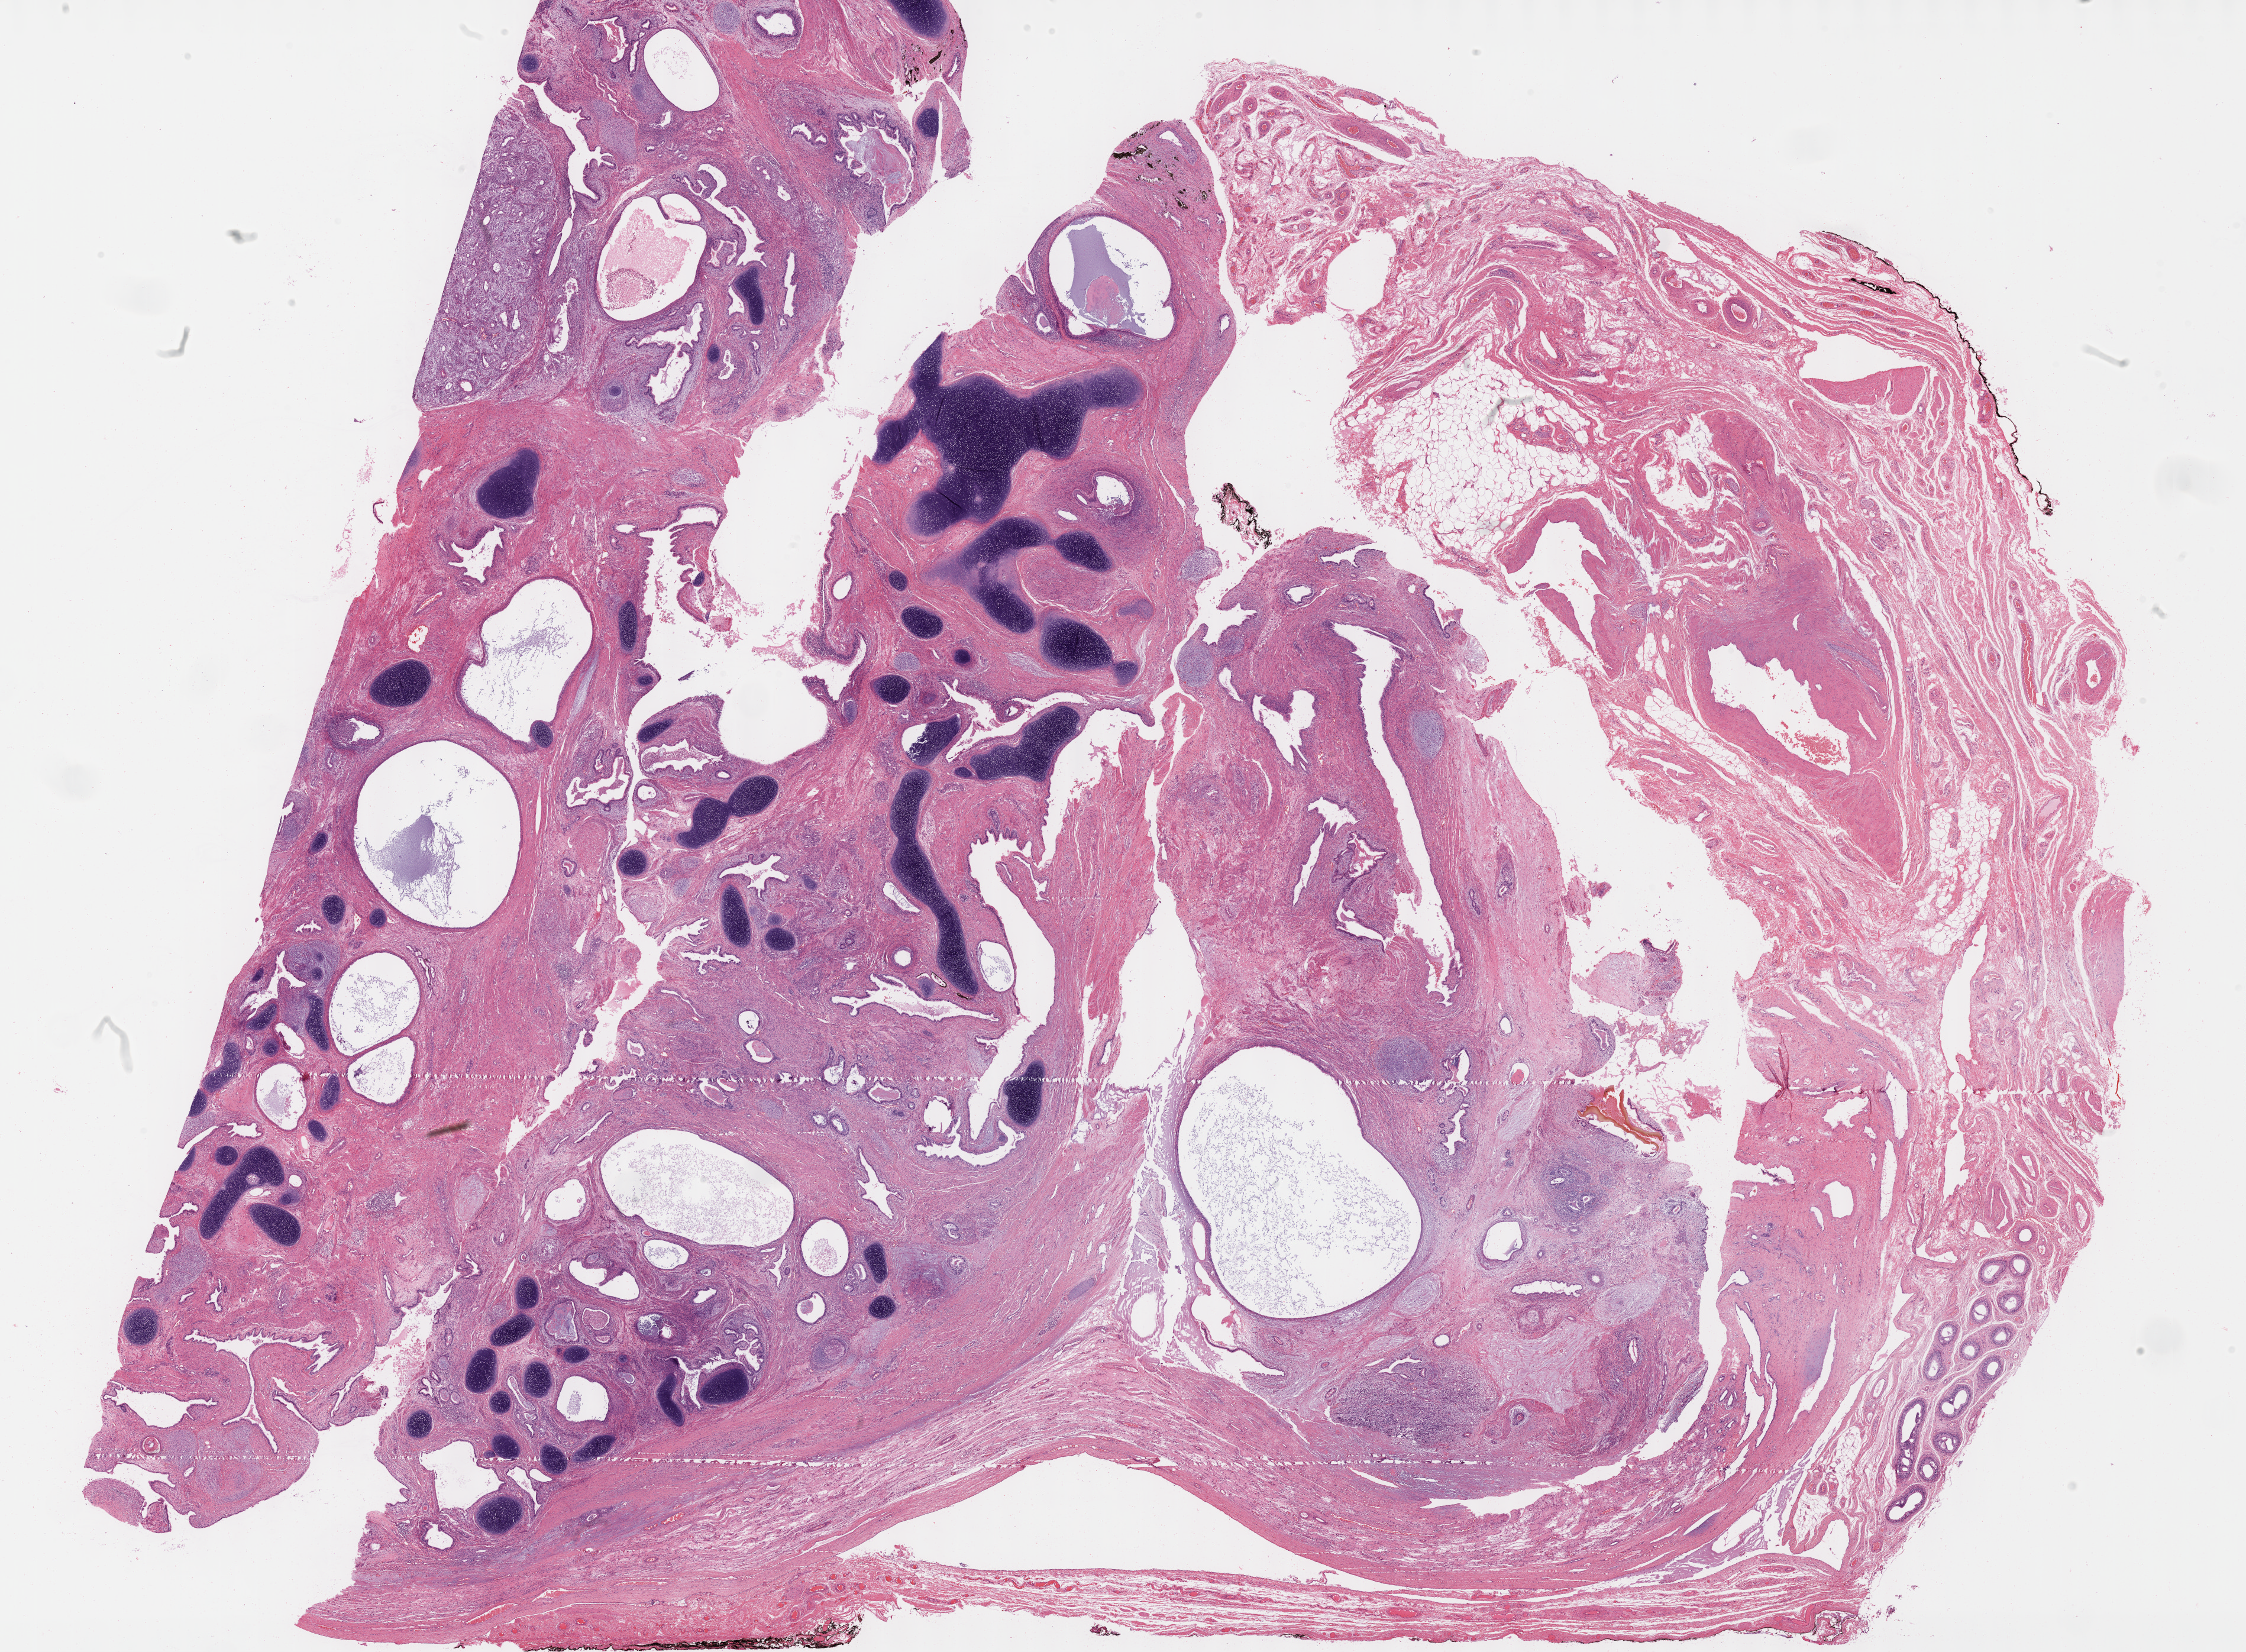
Whole-slide histology image, H&E — low-resolution overview of the scanned area, about 30.7 x 22.6 mm, formalin-fixed paraffin-embedded (FFPE) diagnostic section, sample: primary tumour, testis. Male, age 31 years at initial diagnosis.
Histologic diagnosis: Teratoma, malignant, NOS.